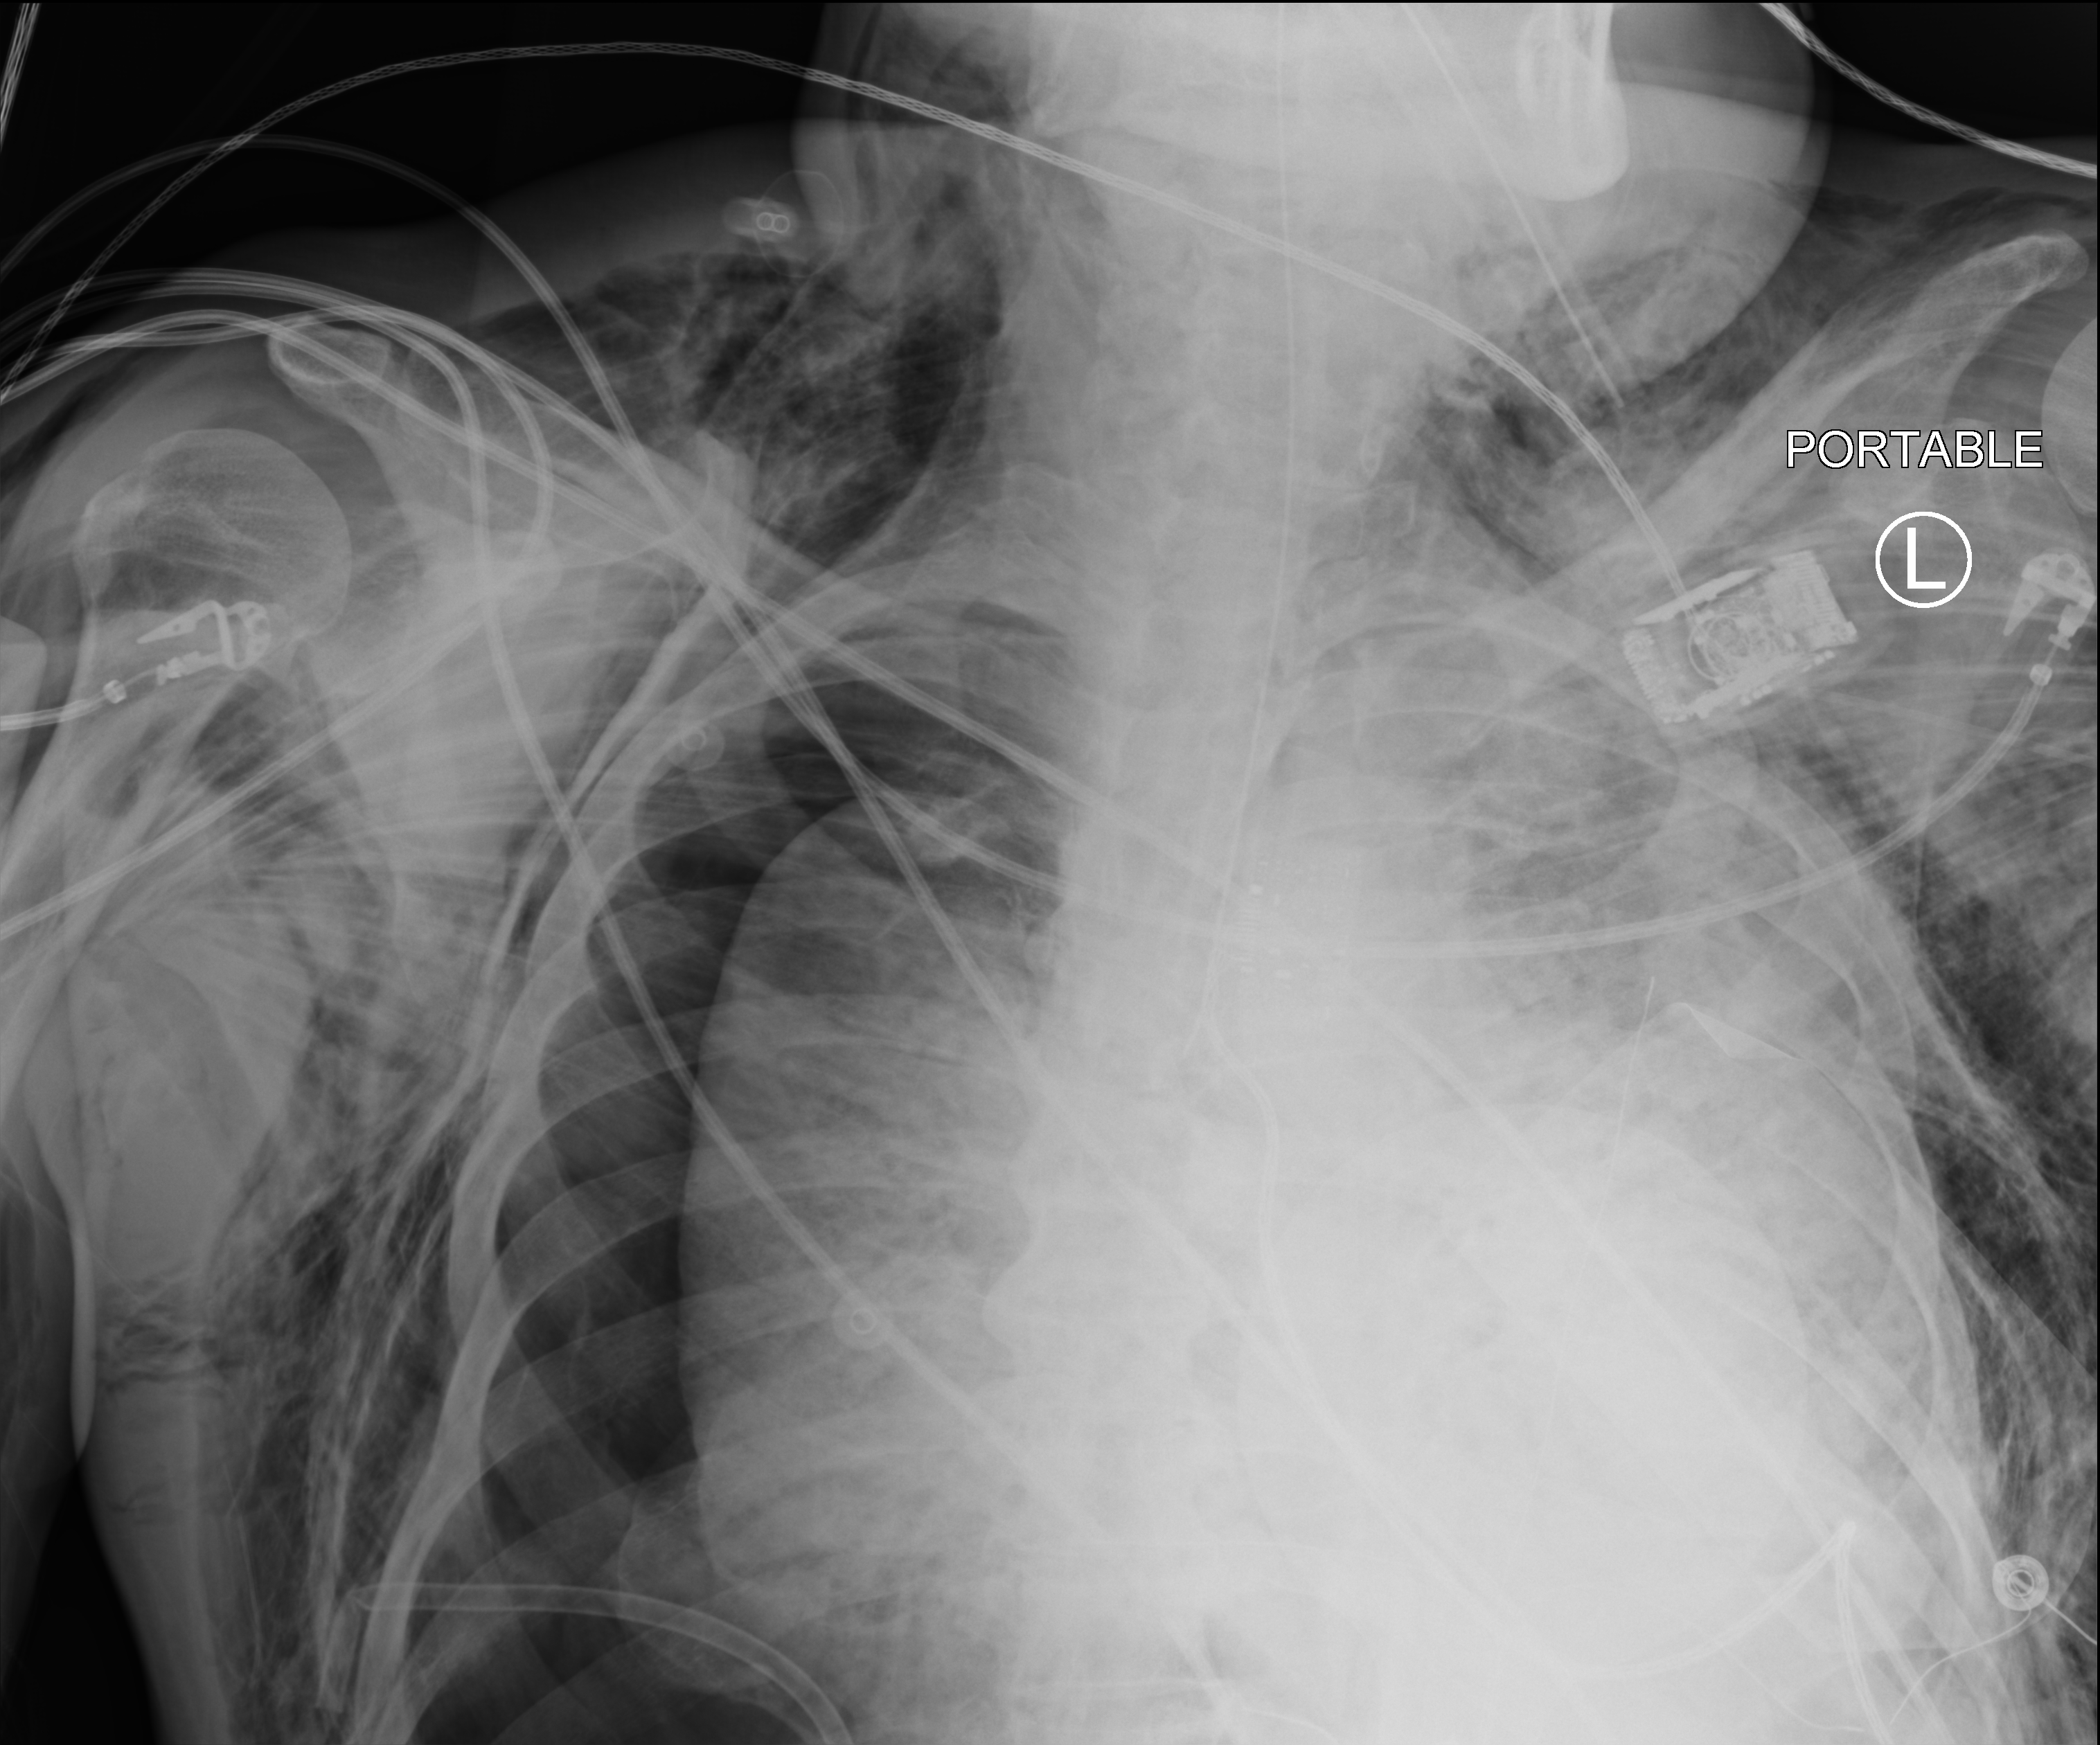
Bedside chest radiograph (computed radiography); anteroposterior (AP) projection. Male patient hospitalised with COVID-19, age 75–90 years.
Admission-level facts for this patient (not findings on this image; timing relative to this image not recorded): diabetes (admission record): no.